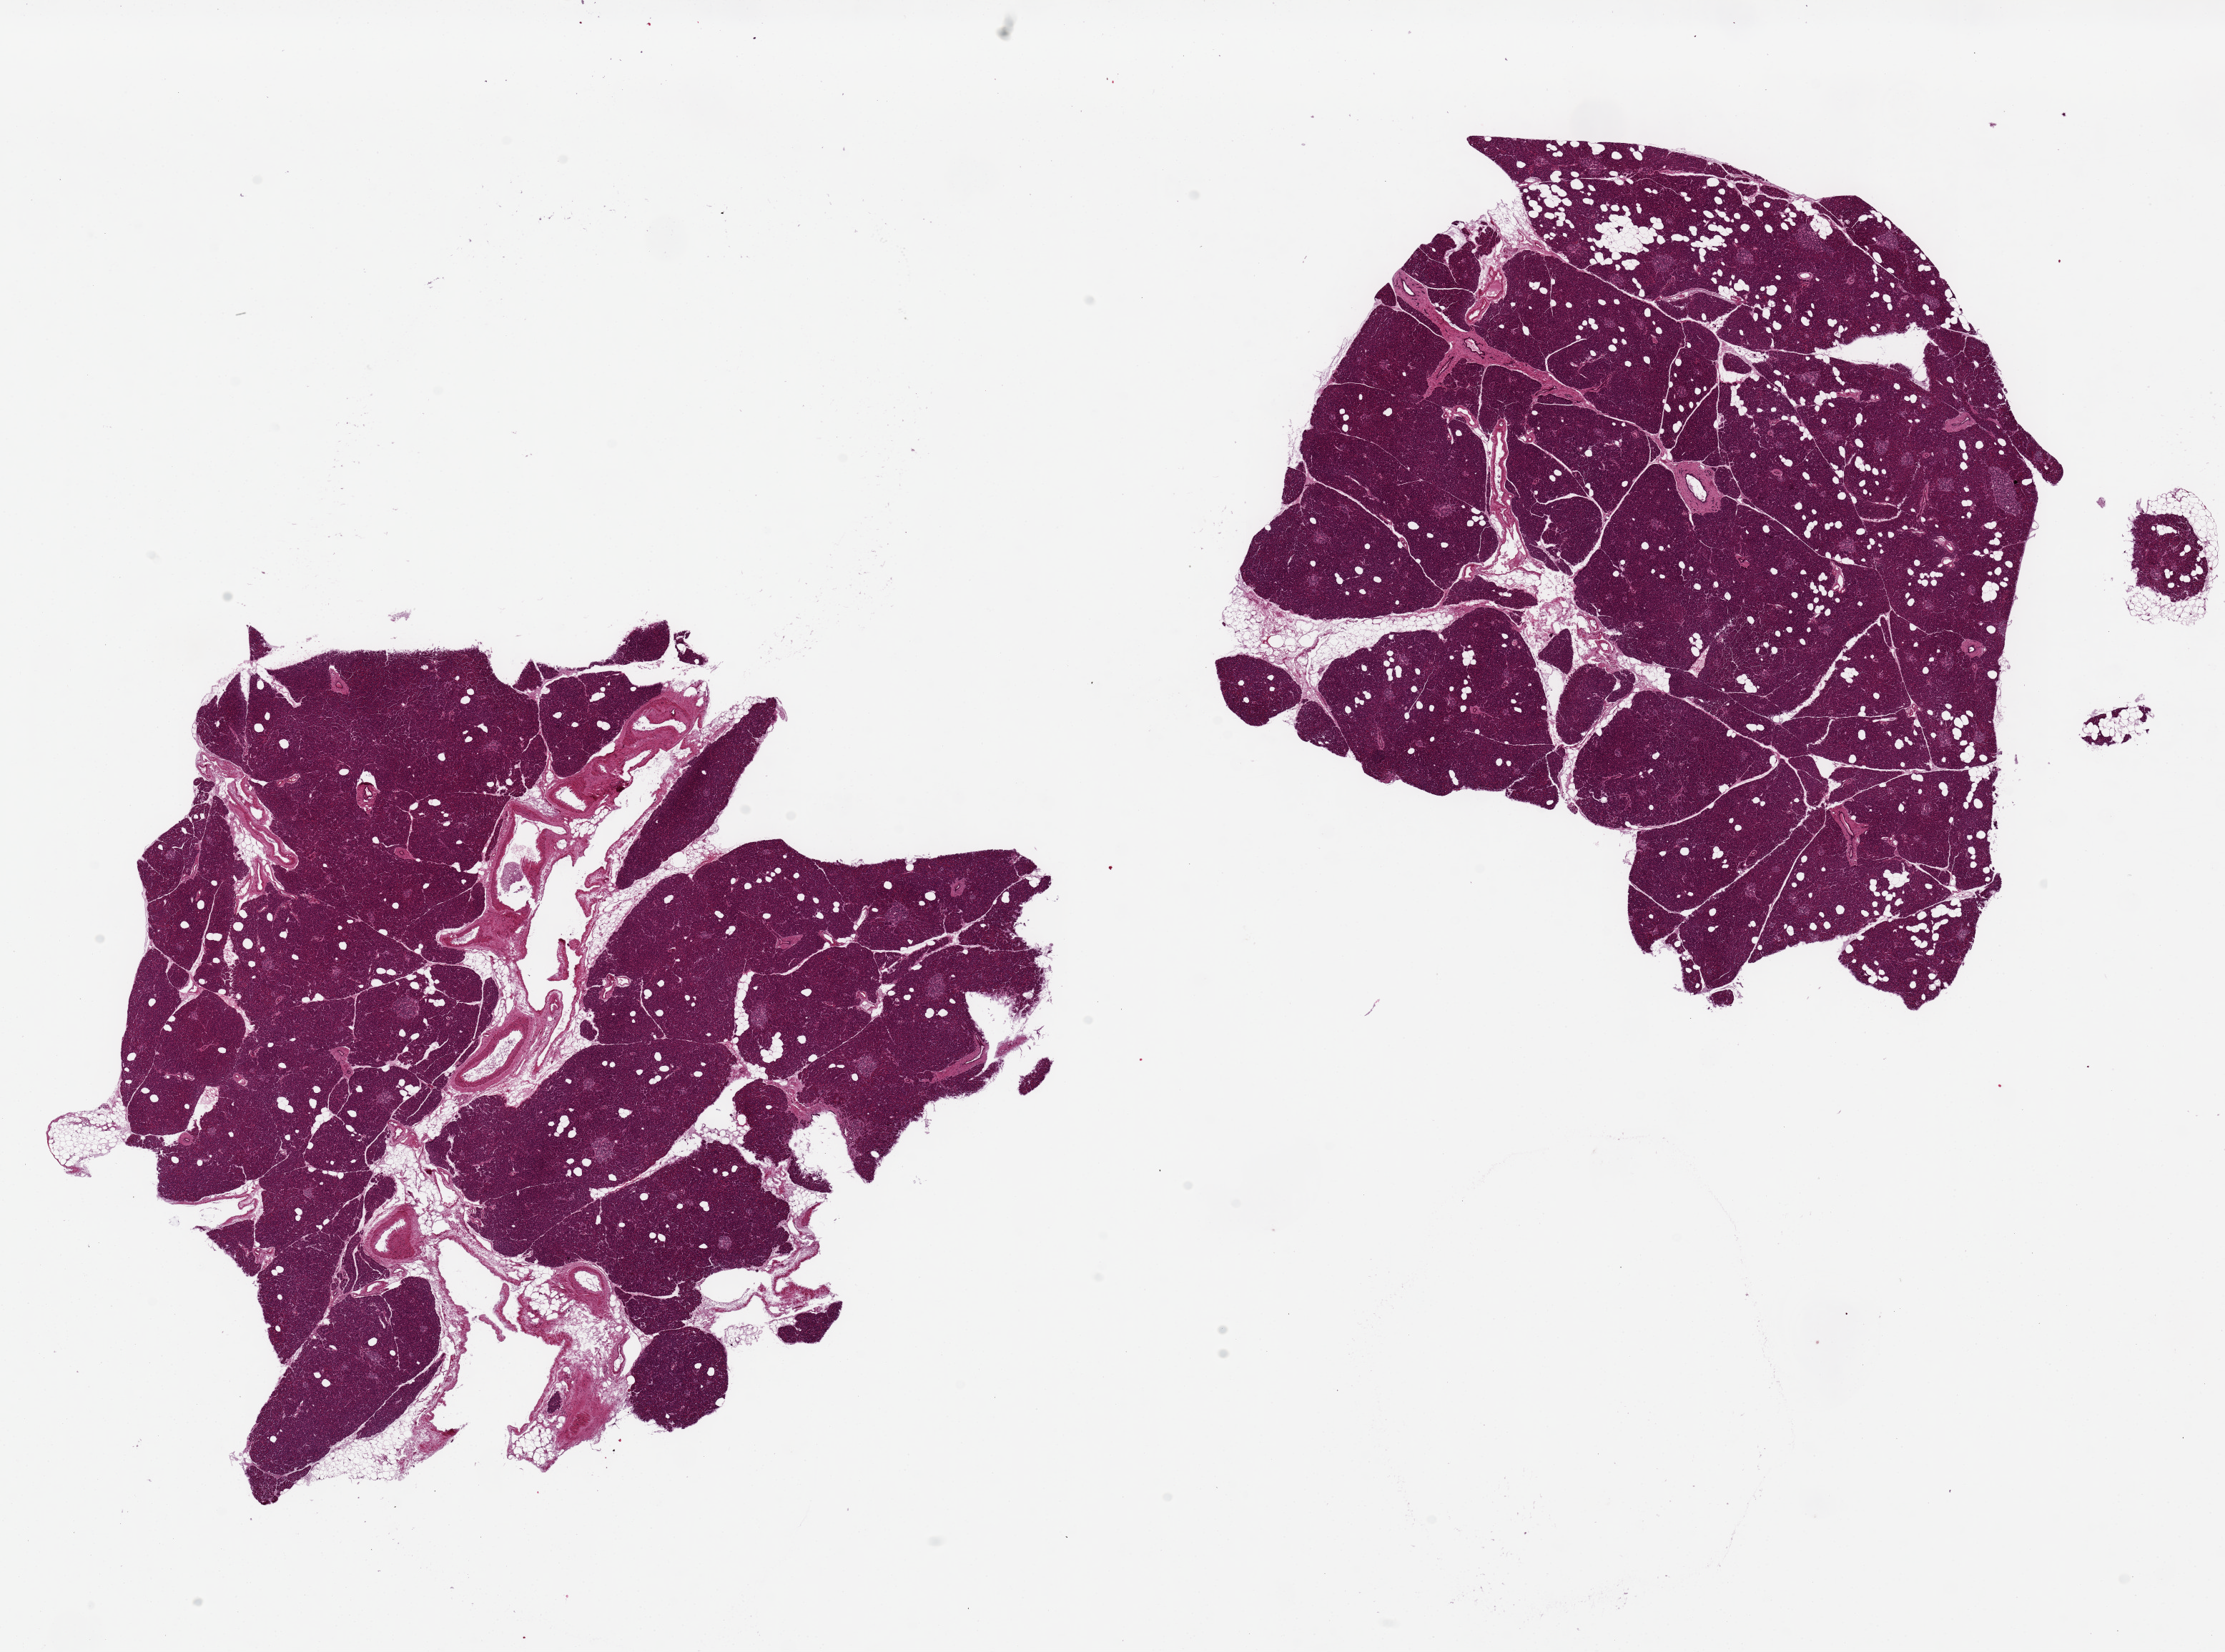
H&E whole-slide image — a low-resolution overview of the entire scanned area, about 24.6 x 18.3 mm (acquisition: 20x scan); PAXgene-fixed, paraffin-embedded tissue; section of pancreas (target tissue); tissue donor sample.
Pathologist's review note for this sample: 2 pieces ~9mm square; scattered adipose cells throughout, <10%.